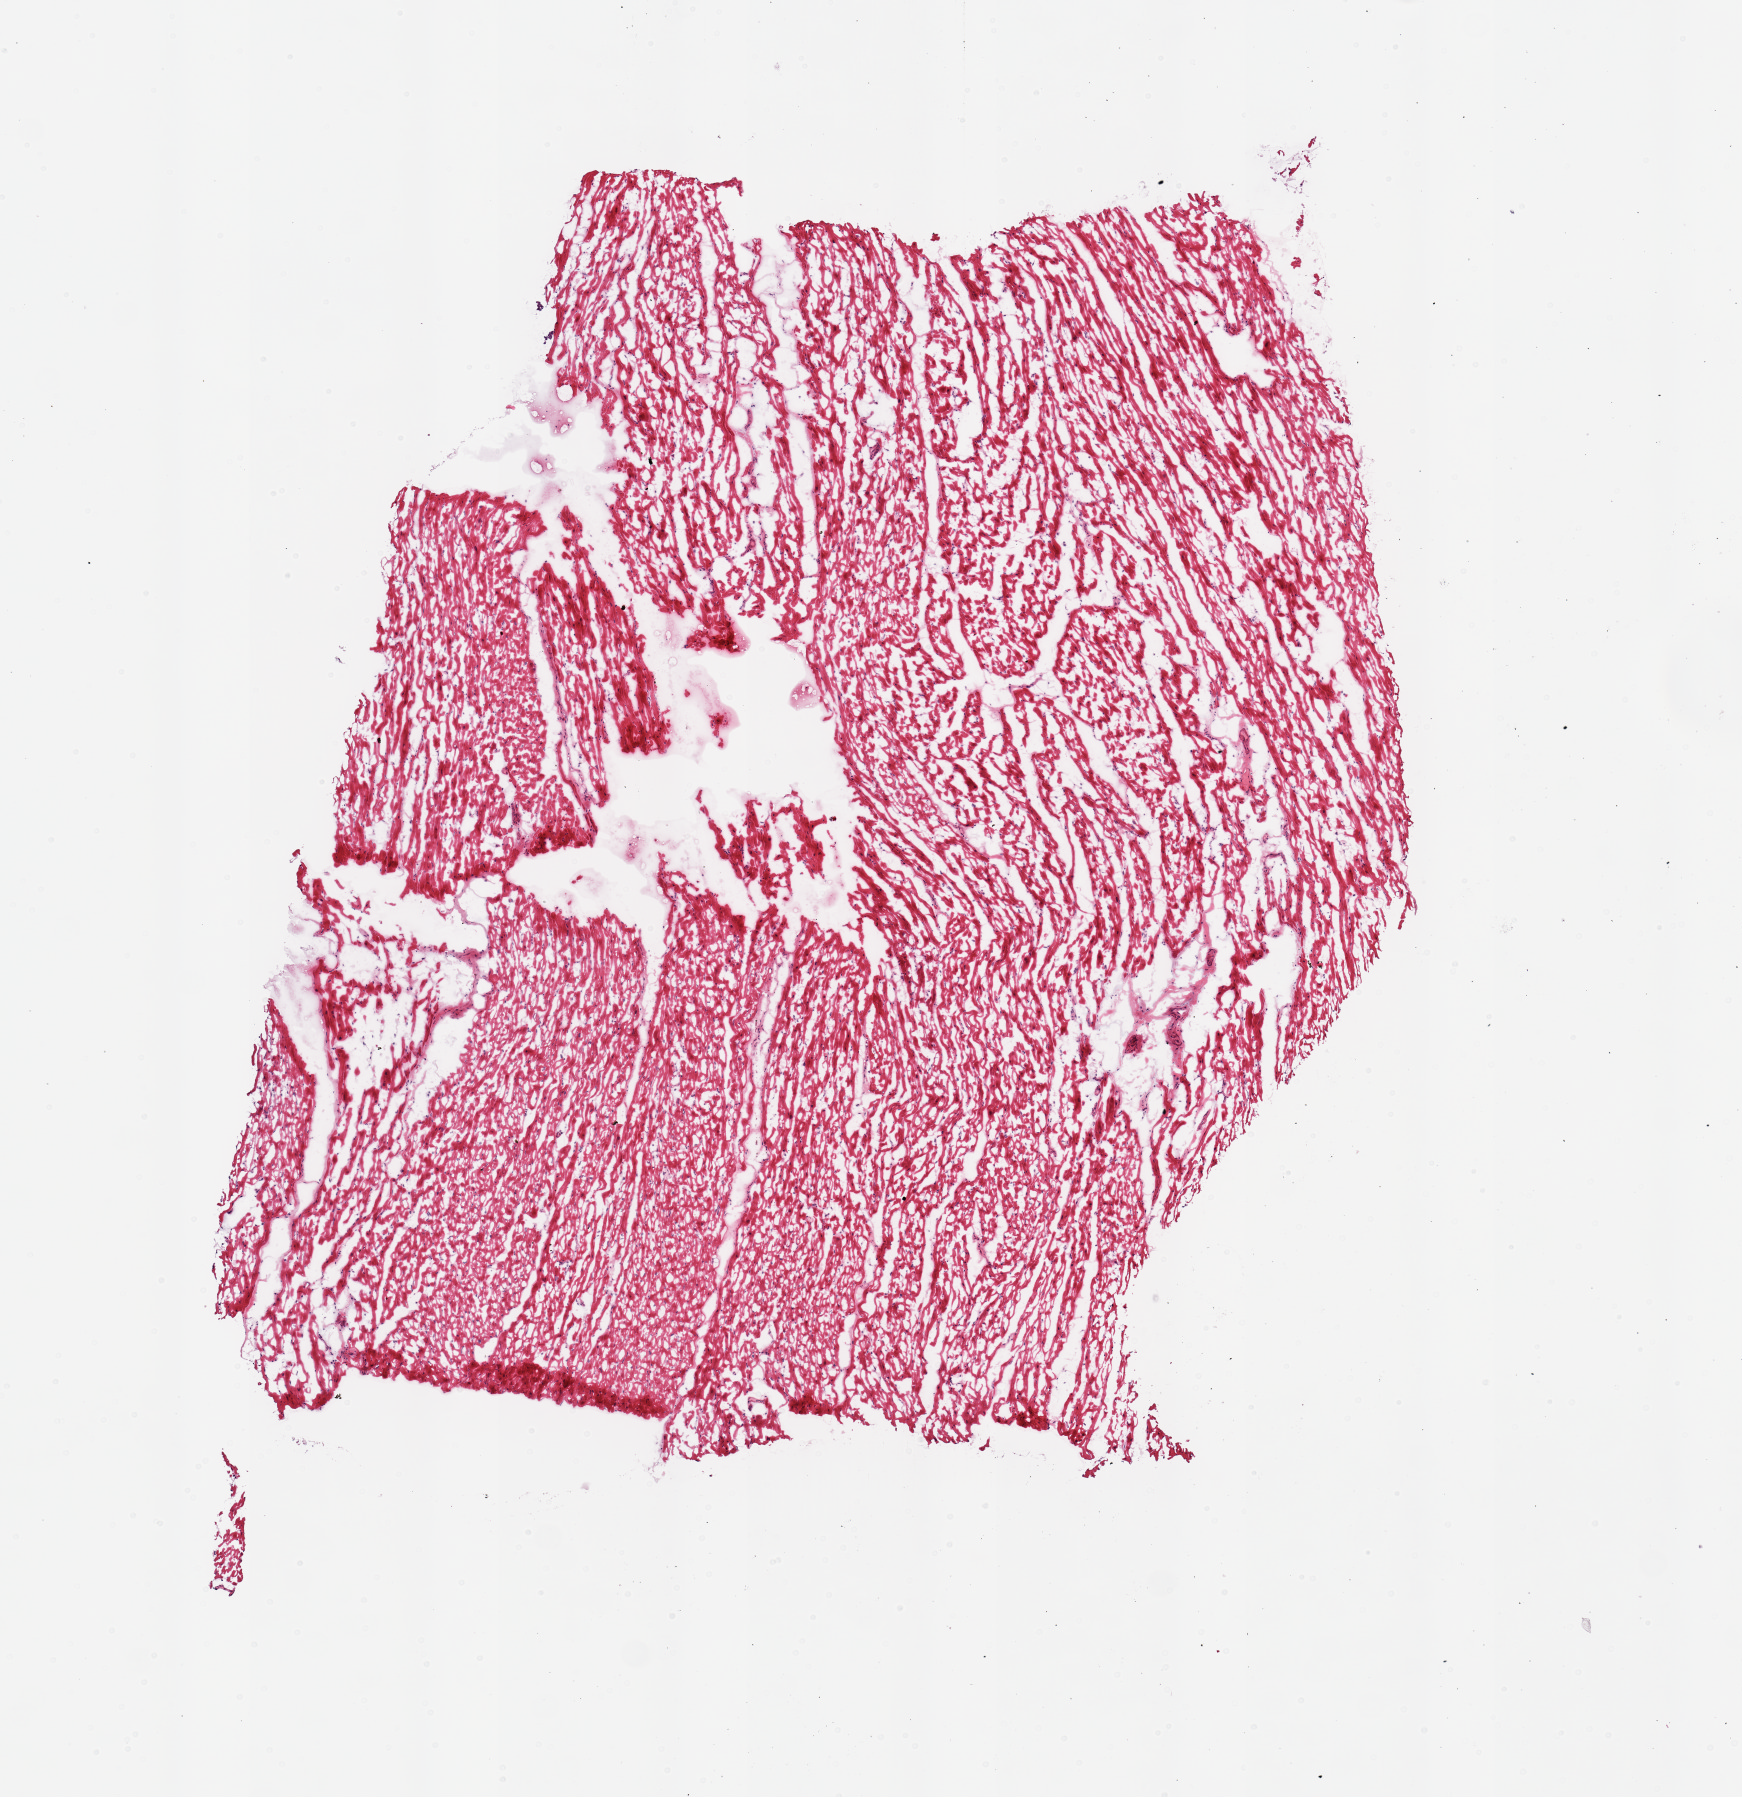
Digitized hematoxylin and eosin (H&E)-stained section, brightfield, a low-resolution overview of the entire scanned area, about 6.9 x 7.1 mm; frozen section; sampled site (target tissue): heart; donor tissue sample. Male donor.
Review note (as recorded): 1 piece.